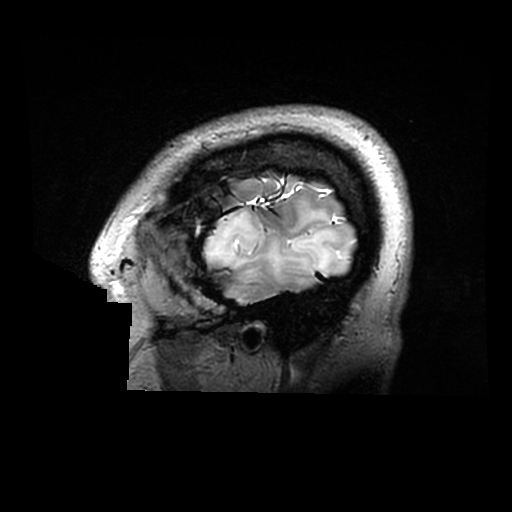
Brain MRI from a brain-tumour surgery series, one sagittal slice. Position 252 of 320 along the scan axis. 0.6 mm slice thickness. 512 × 512 image matrix, field of view 240 × 240 mm. Case-level facts recorded for this patient, not image findings: histopathology: Astrocytoma; WHO grade: 2; IDH mutation: yes.
Annotated regions visible in this slice (expert manual segmentation):
- tumour: bounding box (x1, y1, x2, y2) in pixels: (202, 208, 348, 284)